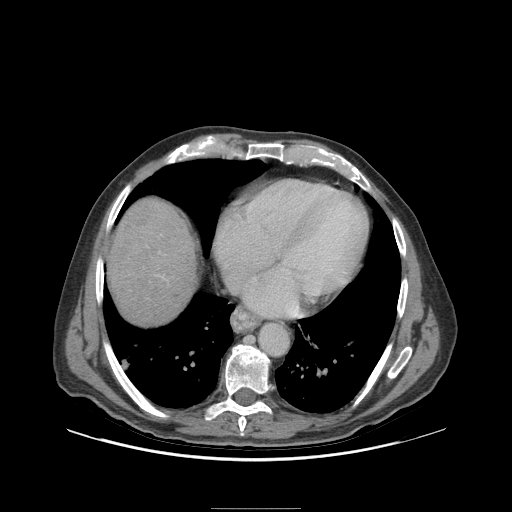
Contrast-enhanced abdominal CT (liver protocol), one axial slice. Slice 92 of 105 in the series (ordered by position). Reconstruction kernel STANDARD. Soft-tissue window (W 400 / L 40 HU). 2.5 mm slice thickness. 512 × 512 image matrix, field of view 440 × 440 mm. Case-level facts recorded for this patient, not image findings: diagnosis: hepatocellular carcinoma (patient treated with transarterial chemoembolisation; whether this scan precedes or follows treatment is not stated here); TNM stage (as recorded): Stage-I; Child-Pugh class: A; tumour nodularity: uninodular; tumour size: 5.1 cm.
Annotated regions visible in this slice (semi-automatic segmentation, software-assisted and operator-edited):
- liver parenchyma outside the tumour (the mass and vessels are separate outlines, so this box may not span the whole liver): bounding box <108,198,196,324> (left, top, right, bottom; pixels)